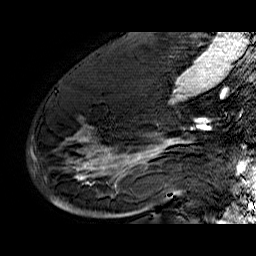
Breast MRI (dynamic contrast-enhanced), one sagittal slice. Position 35 of 60 along the scan axis. Dynamic contrast-enhanced series, time point 2 of 6 at this slice position (early post-contrast). 1.5 T. TE 6.4 ms, TR 32.9 ms. 256 × 256 image matrix. Female patient. Case-level facts recorded for this patient, not image findings: setting: breast cancer imaged before/during neoadjuvant chemotherapy; receptor status: HR-positive, HER2-negative.
Outlined on this slice (semi-automatic segmentation, software-assisted and operator-edited):
- analysis volume of interest (the breast-tissue region the enhancement analysis was run in; not a lesion): bounding box (x1, y1, x2, y2) in pixels: (52, 74, 176, 210)
- tumour enhancement mask (voxels above the 100 % enhancement threshold inside the analysis volume of interest): (56, 92, 176, 202)